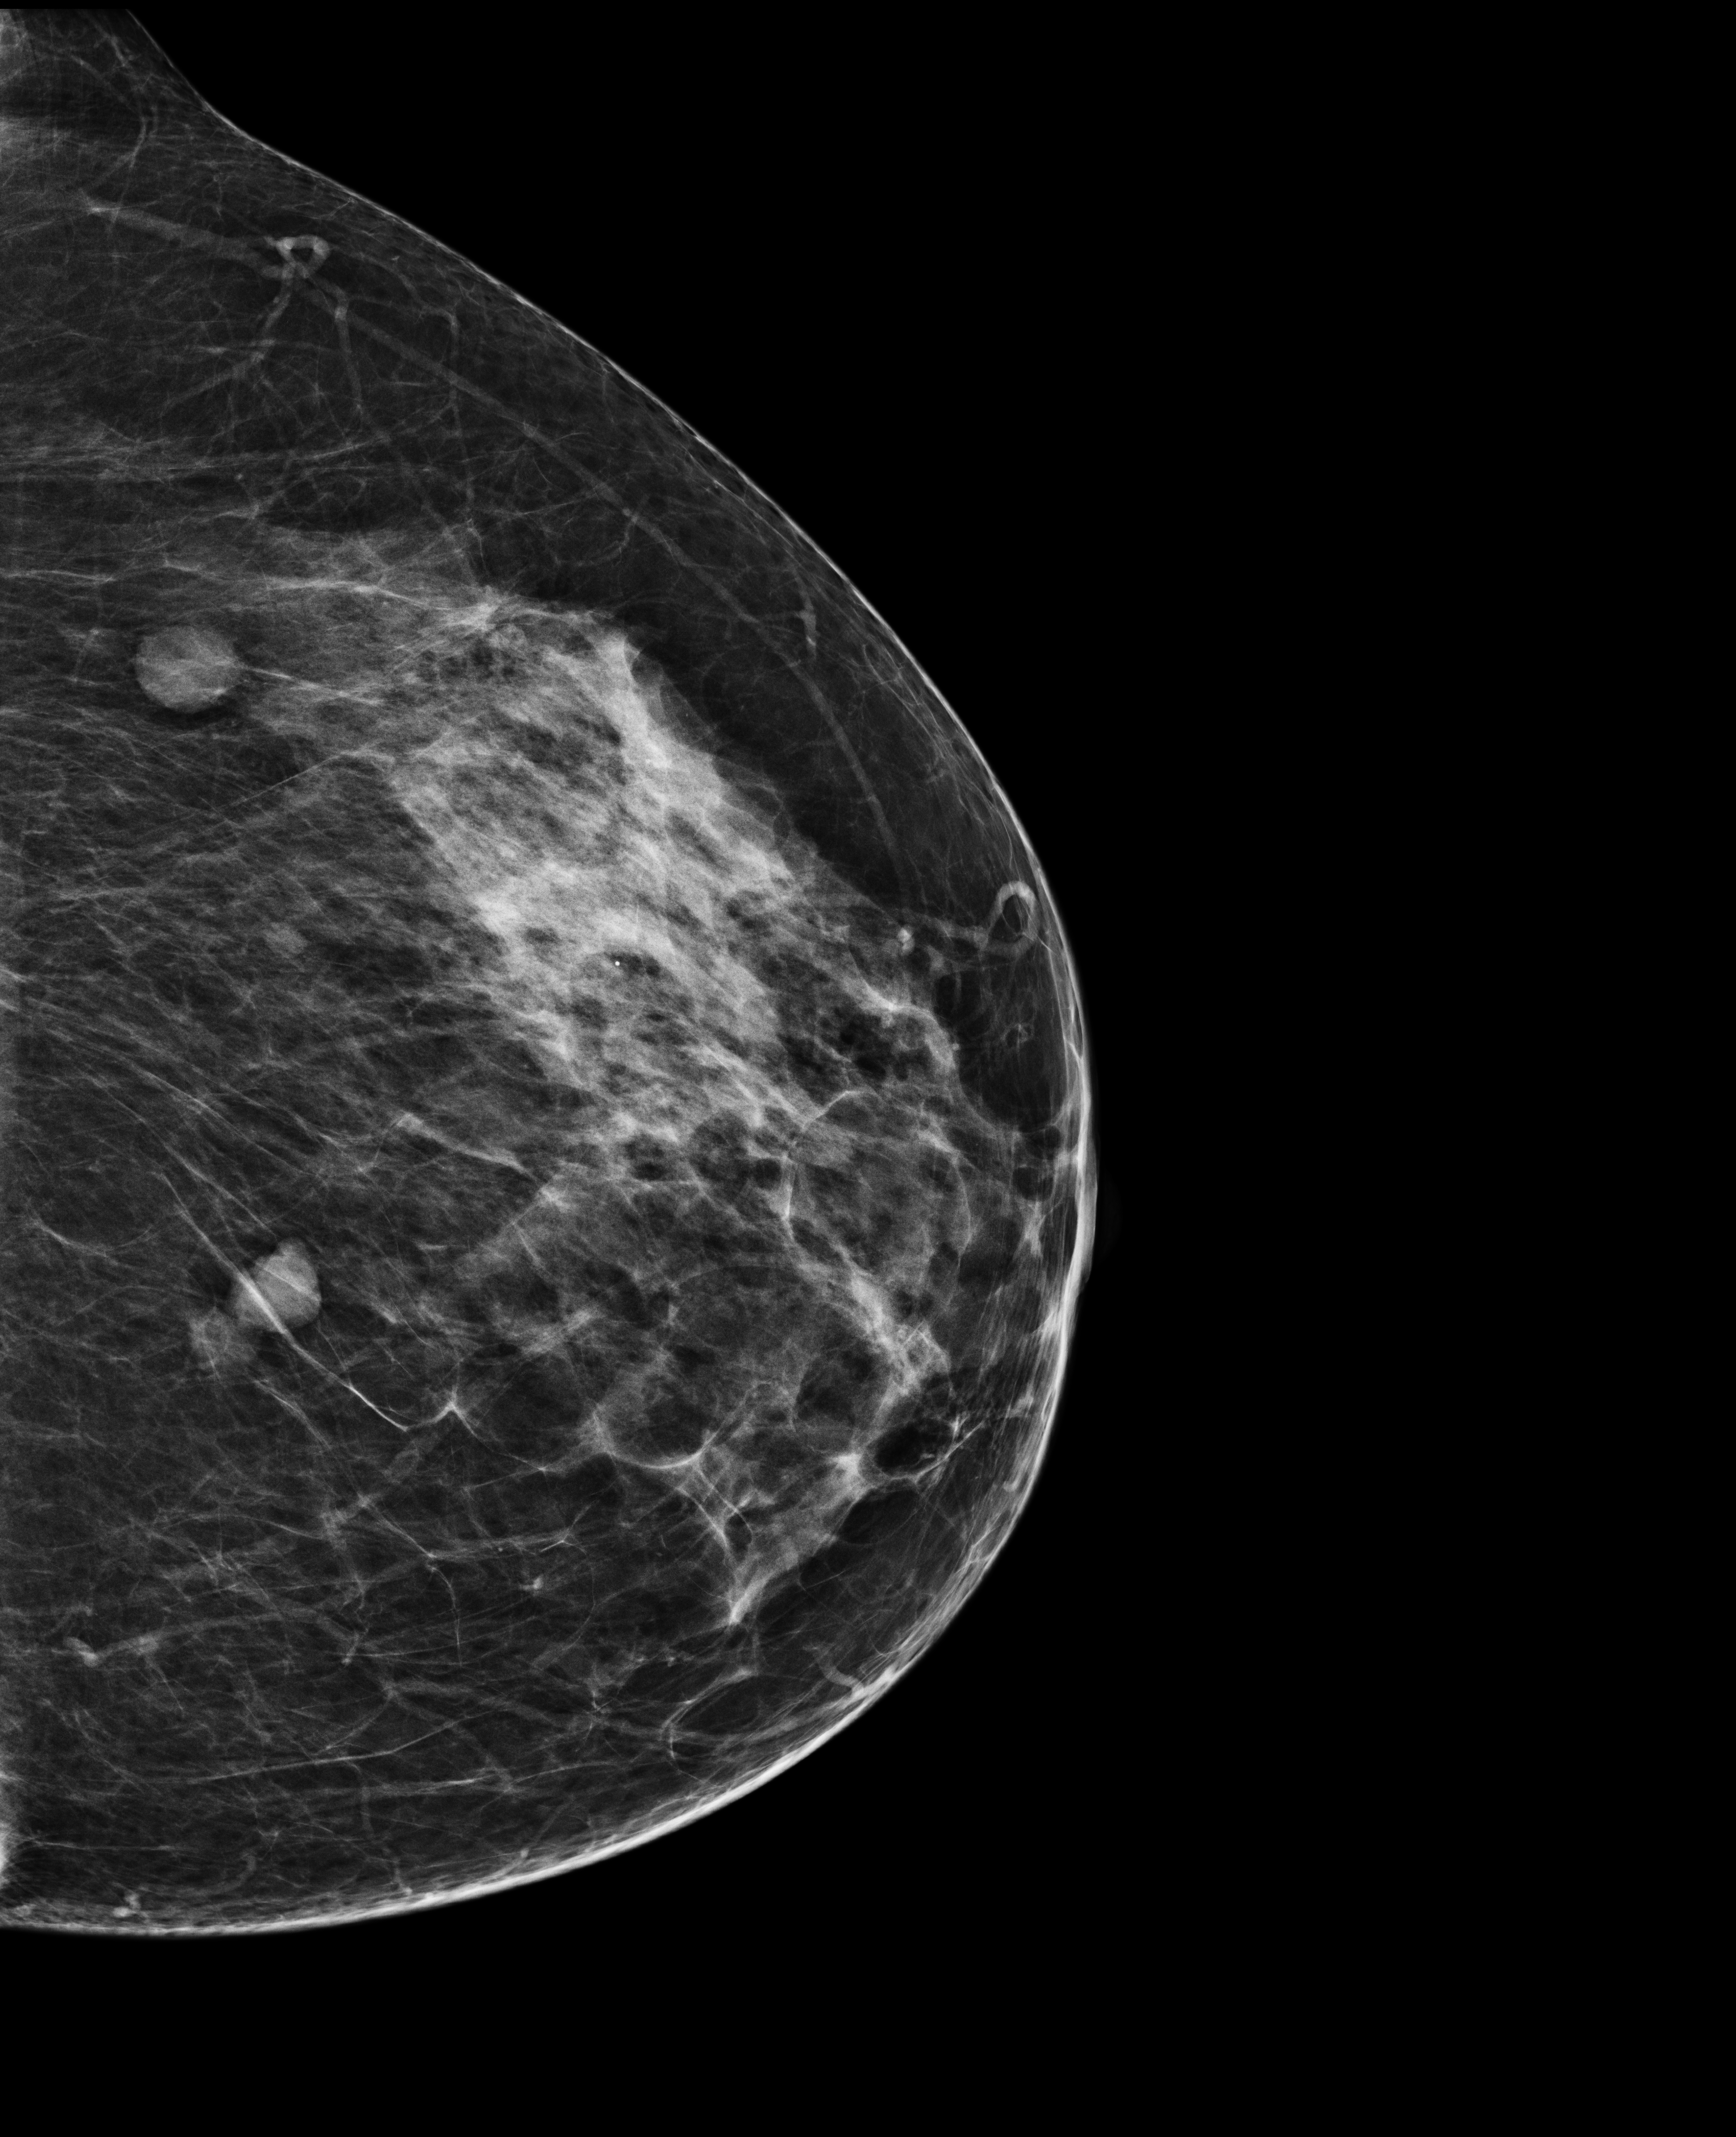
Annual screening mammography examination; compressed breast thickness 69 mm. Patient: female, 49 years.
Image type: full-field digital mammogram. Breast: left. Projection: cranio-caudal projection.